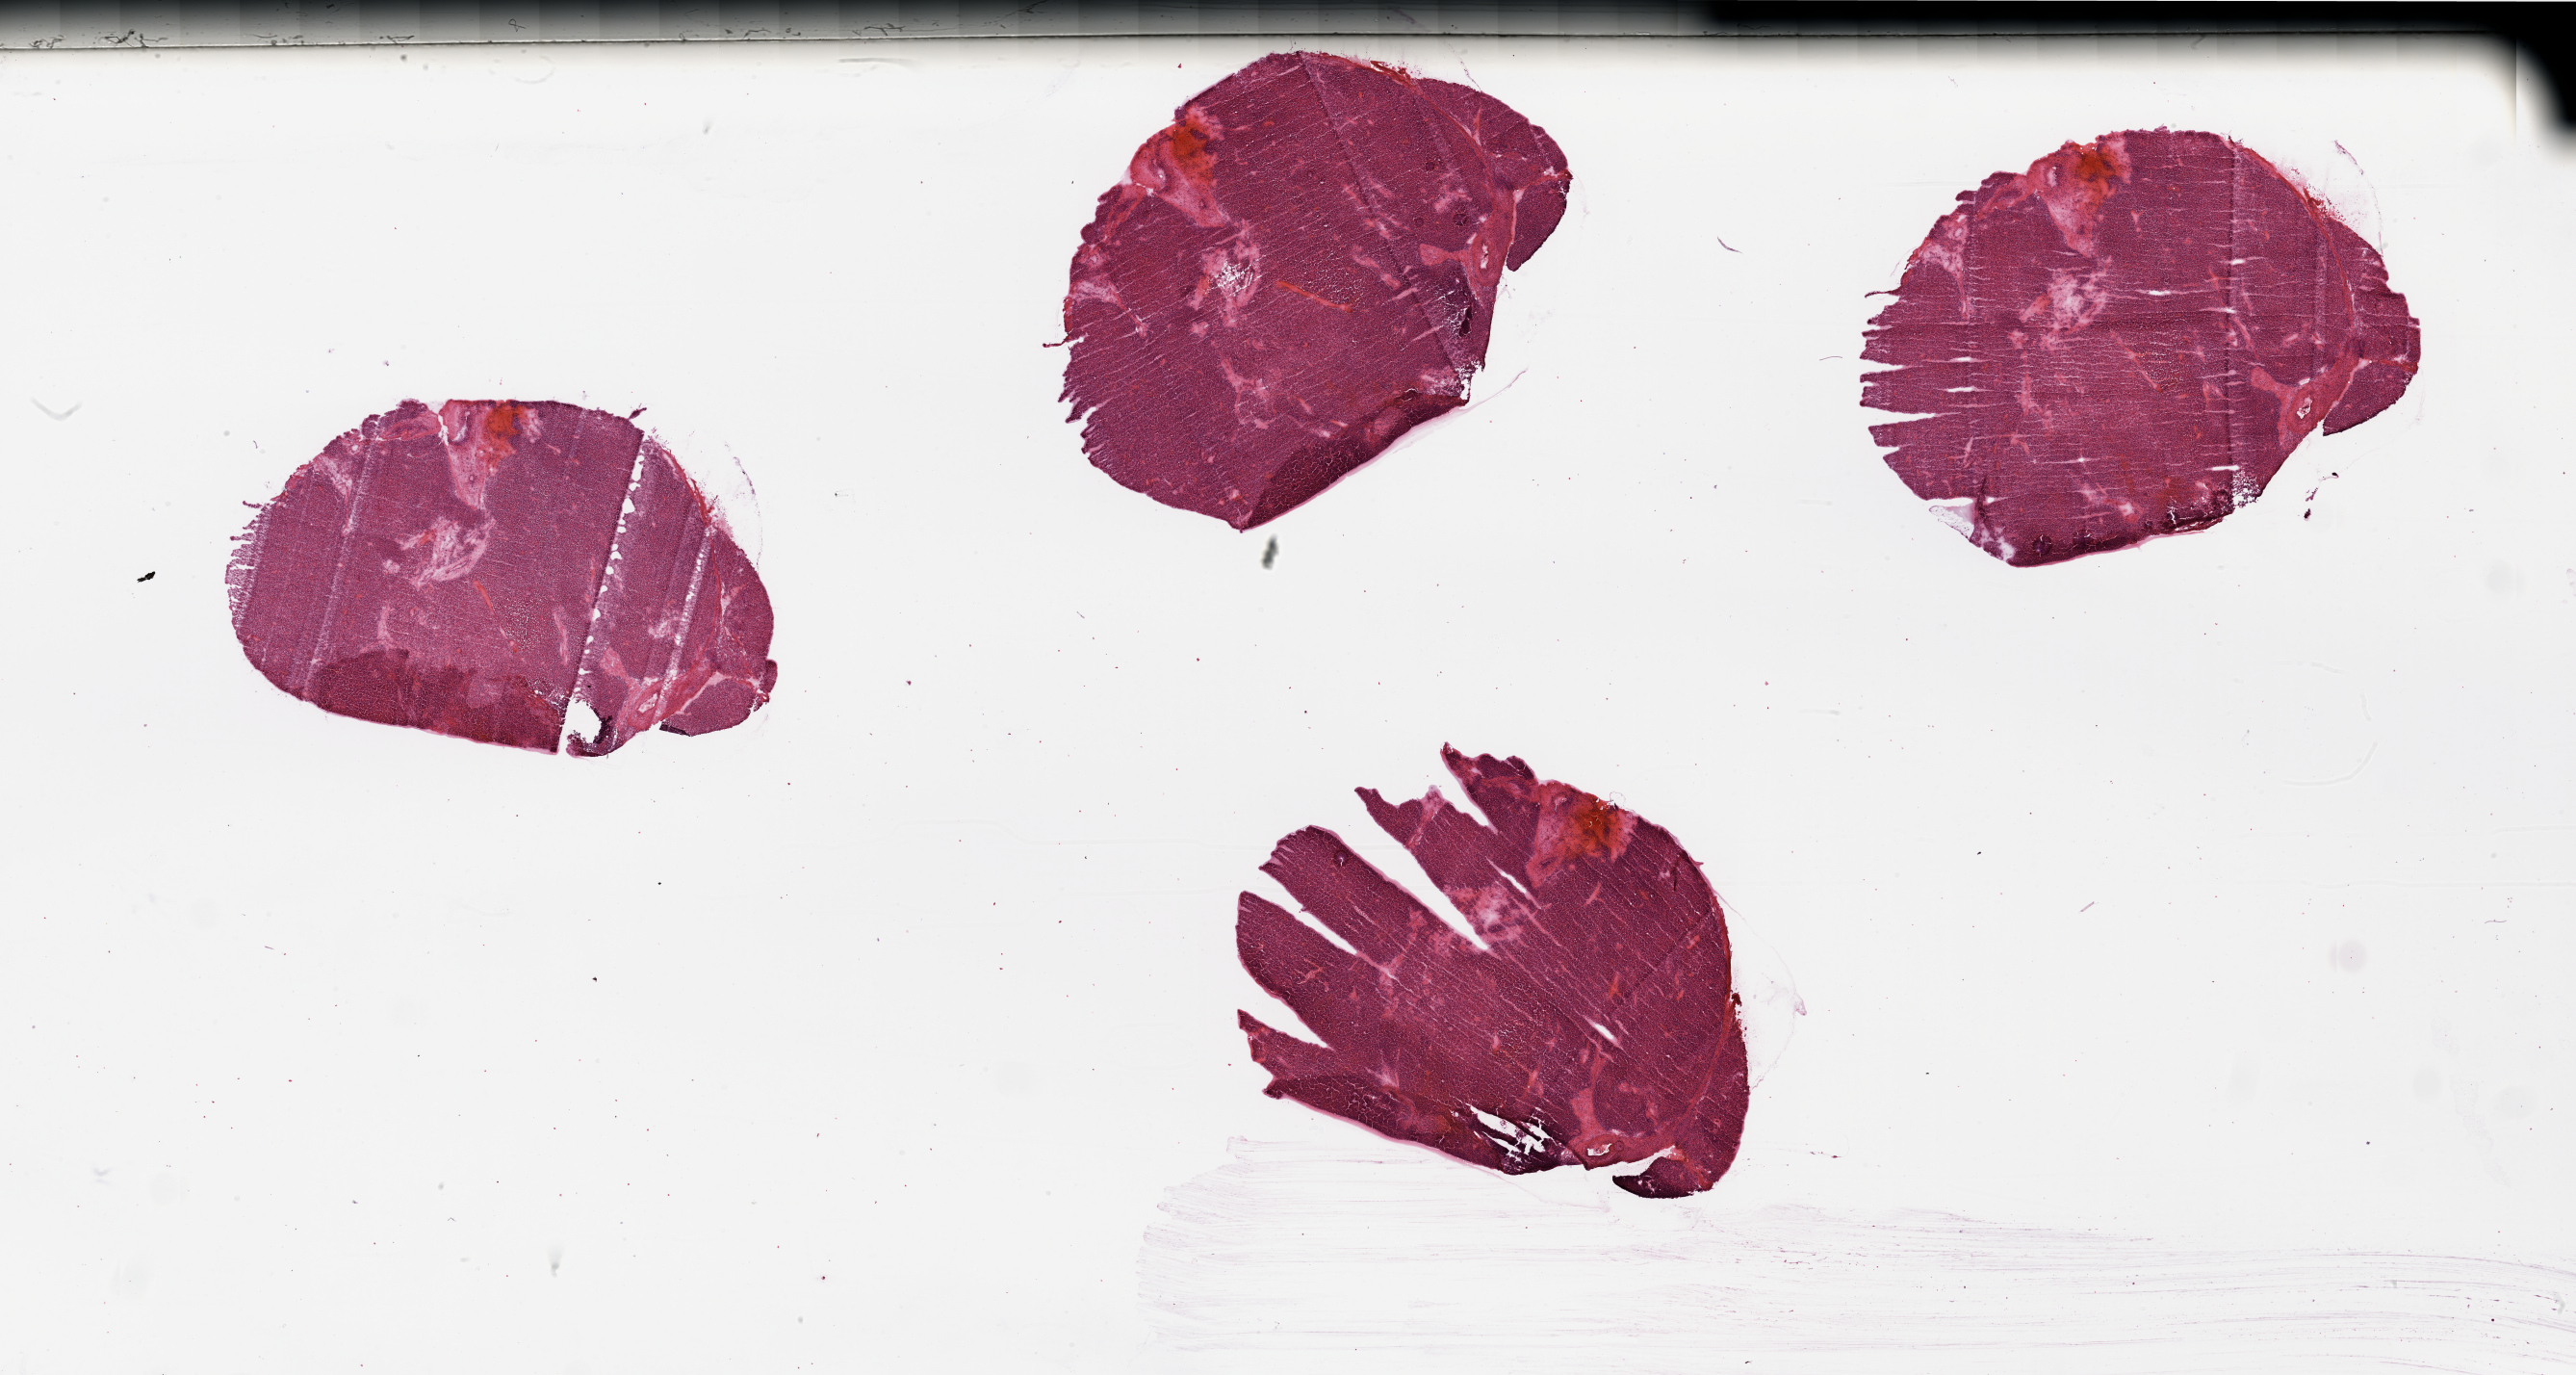
H&E-stained whole-slide image, low-resolution overview of the scanned area, about 42.3 x 22.6 mm (from a 20x scan), tumour tissue sample, sampled site: kidney. Patient: male, age 67 years. Histologic grade: G2 (moderately differentiated). Composition of this section per pathologist review: tumour nuclei 90%, necrosis 5%.
Histologic diagnosis: Renal cell carcinoma, NOS. Primary tumour site (as recorded): middle. AJCC pathologic stage: III.